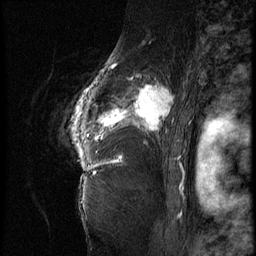
Breast MRI (dynamic contrast-enhanced), one sagittal slice; slice 52 of 62 in the series (ordered by position); 3 images stored at this slice position (order not interpretable as contrast timing); 1.5 T; TE 4.2 ms, TR 9 ms; 2.5 mm slice thickness; 256 × 256 image matrix, field of view 180 × 180 mm. Female patient, age 56 years. Case-level facts recorded for this patient, not image findings: setting: breast cancer imaged before/during neoadjuvant chemotherapy; receptor status: HER2-positive.
Outlined on this slice (semi-automatically segmented with operator editing):
- analysis volume of interest (the breast-tissue region the enhancement analysis was run in; not a lesion): bounding box [x1, y1, x2, y2] px = [84, 75, 181, 153]
- tumour enhancement mask (voxels above the 140 % enhancement threshold inside the analysis volume of interest): [86, 84, 173, 141]